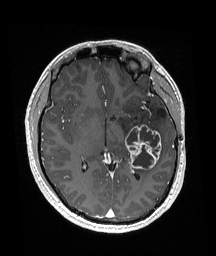
Brain MRI from a brain-tumour surgery series, one axial slice; position 96 of 192 along the scan axis; T1-weighted post-contrast; 1 mm slice thickness; 216 × 256 image matrix, field of view 211 × 250 mm. Case-level facts recorded for this patient, not image findings: histopathology: Glioneuronal tumor; WHO grade: 2; tumour location: Left Superior Temporal Gyrus.
Annotated regions visible in this slice (outlined manually by an expert reader):
- previous resection cavity: bounding box (x1, y1, x2, y2) in pixels: (157, 109, 167, 118)
- tumour: (126, 124, 162, 170)